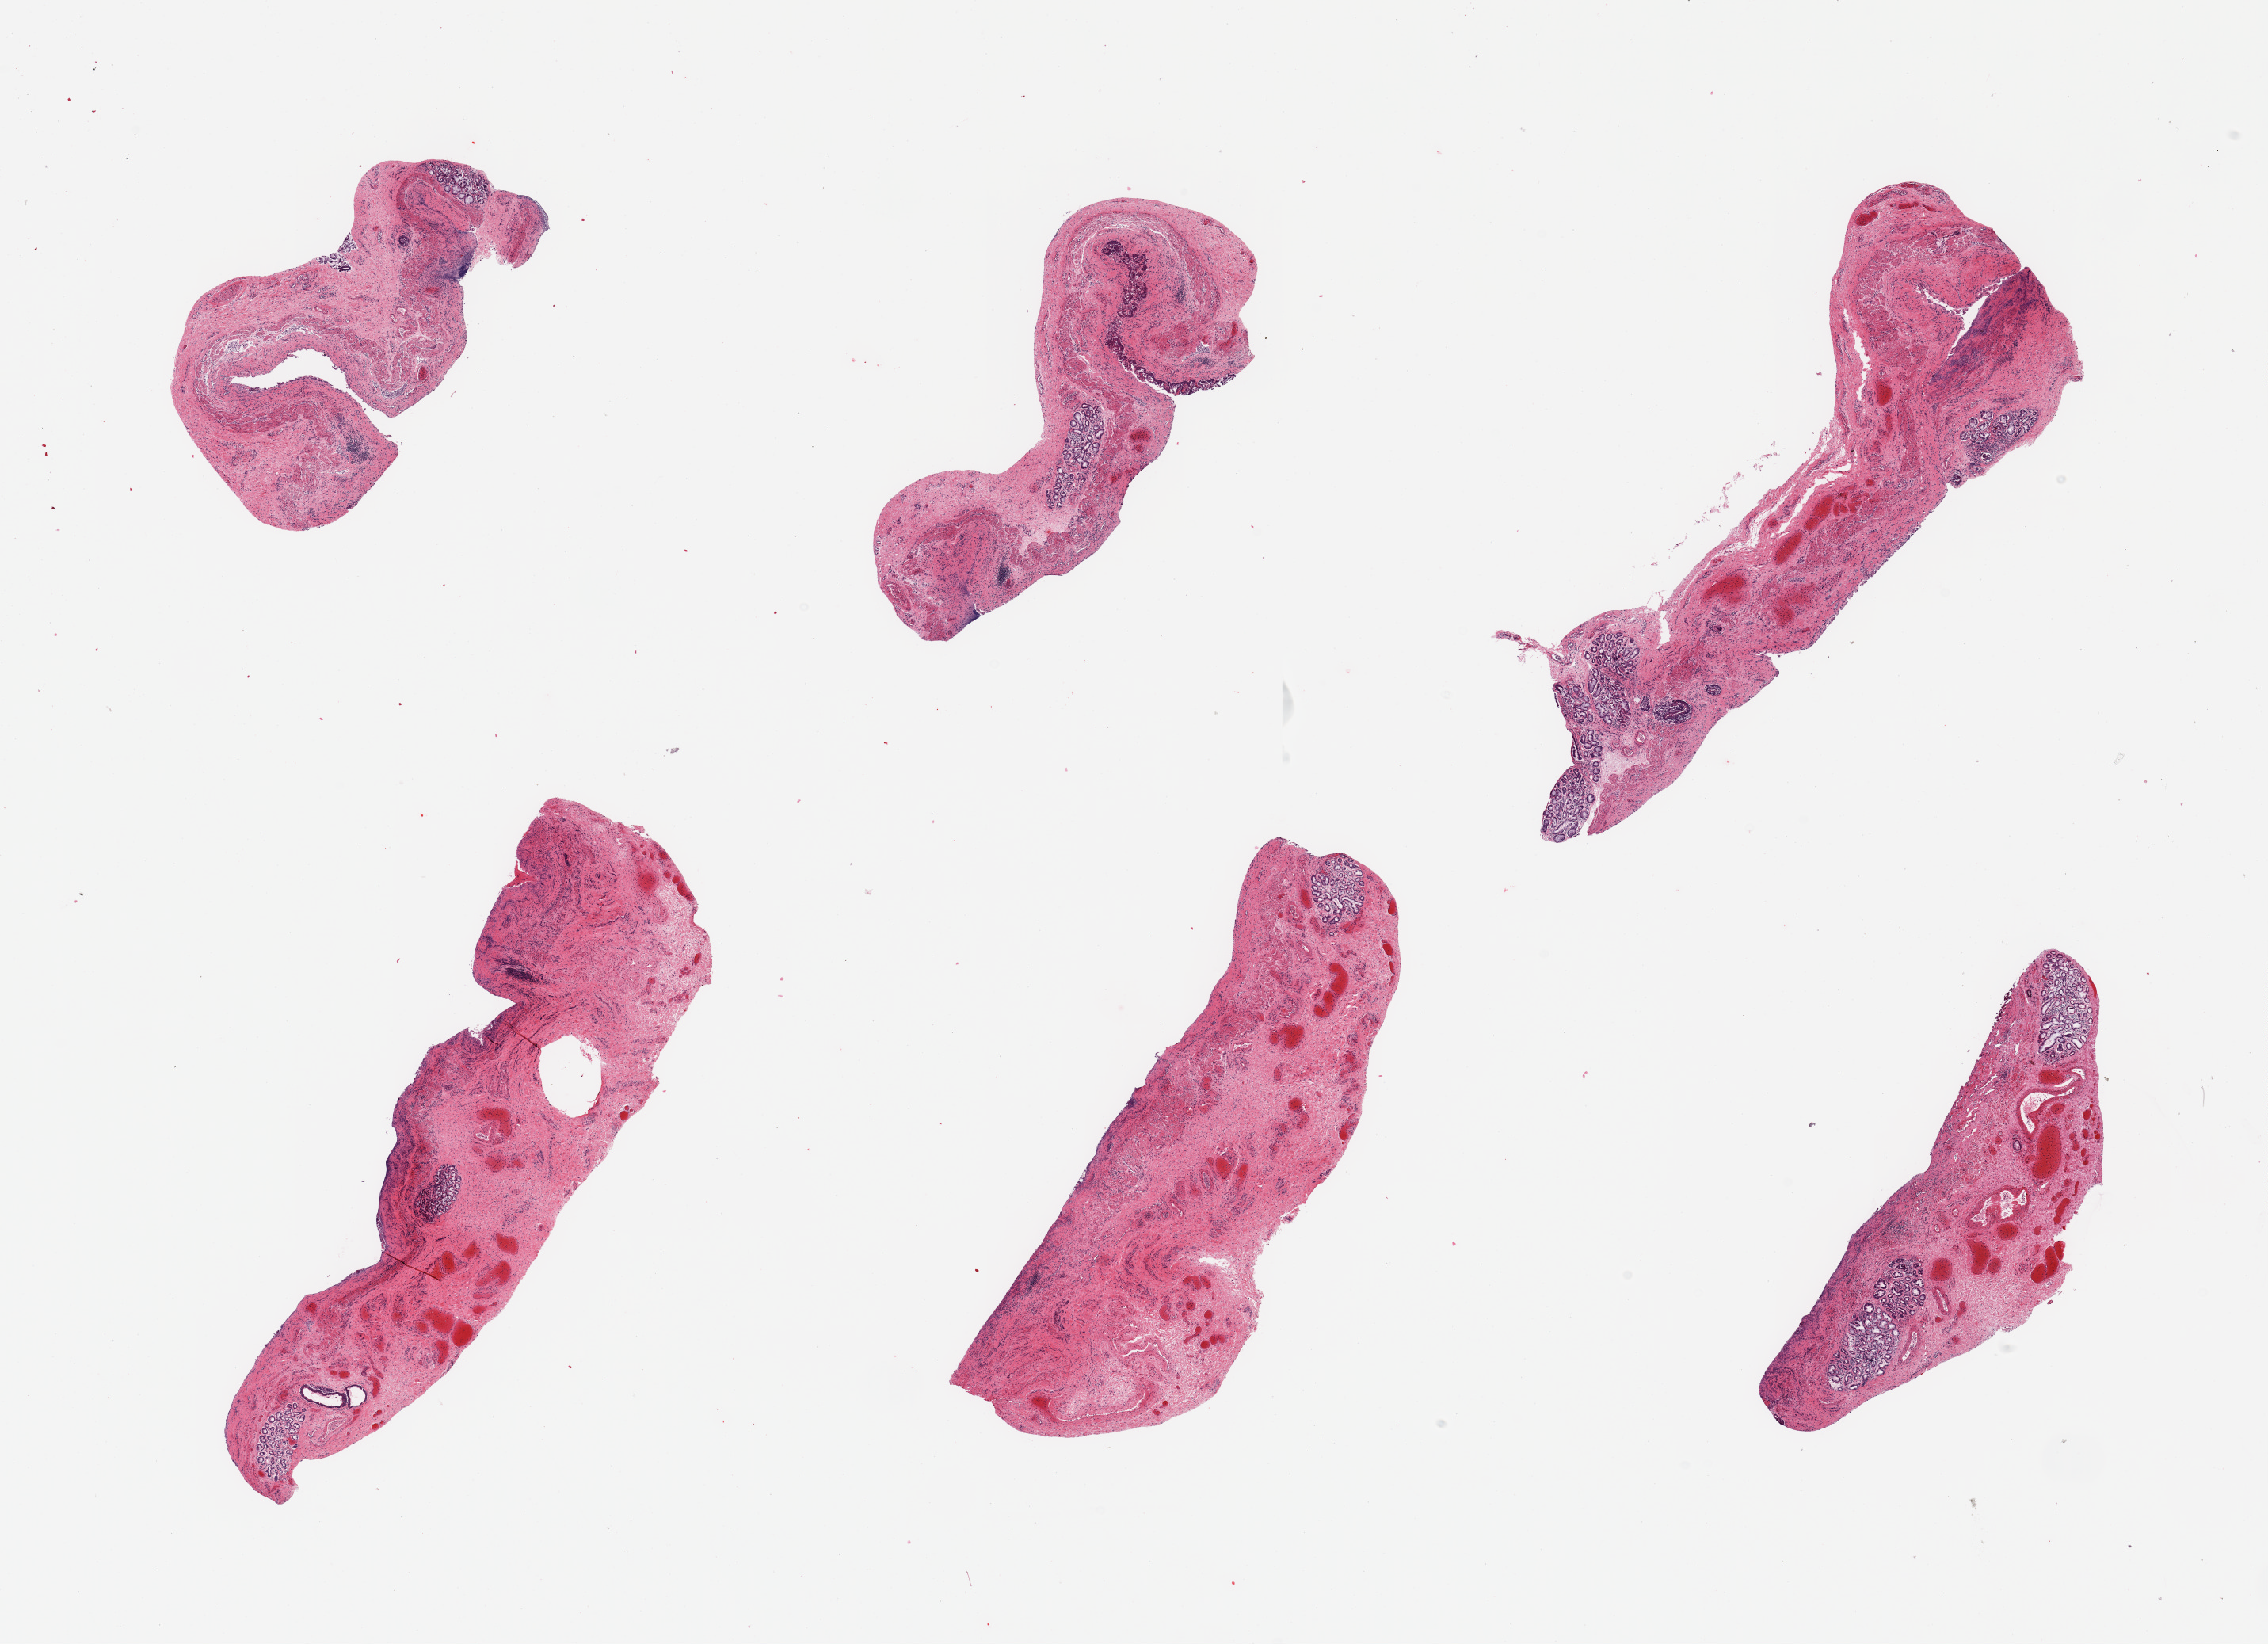
H&E whole-slide image, low-resolution overview of the scanned area, about 22.6 x 16.4 mm; PAXgene-fixed paraffin-embedded (PFPE) section; section of esophageal mucous membrane (target tissue); tissue donor sample. Donor: female.
Review note (as recorded): 6 pieces; surface epithelium largely sloughed; chronic esophagitis (reflux history).